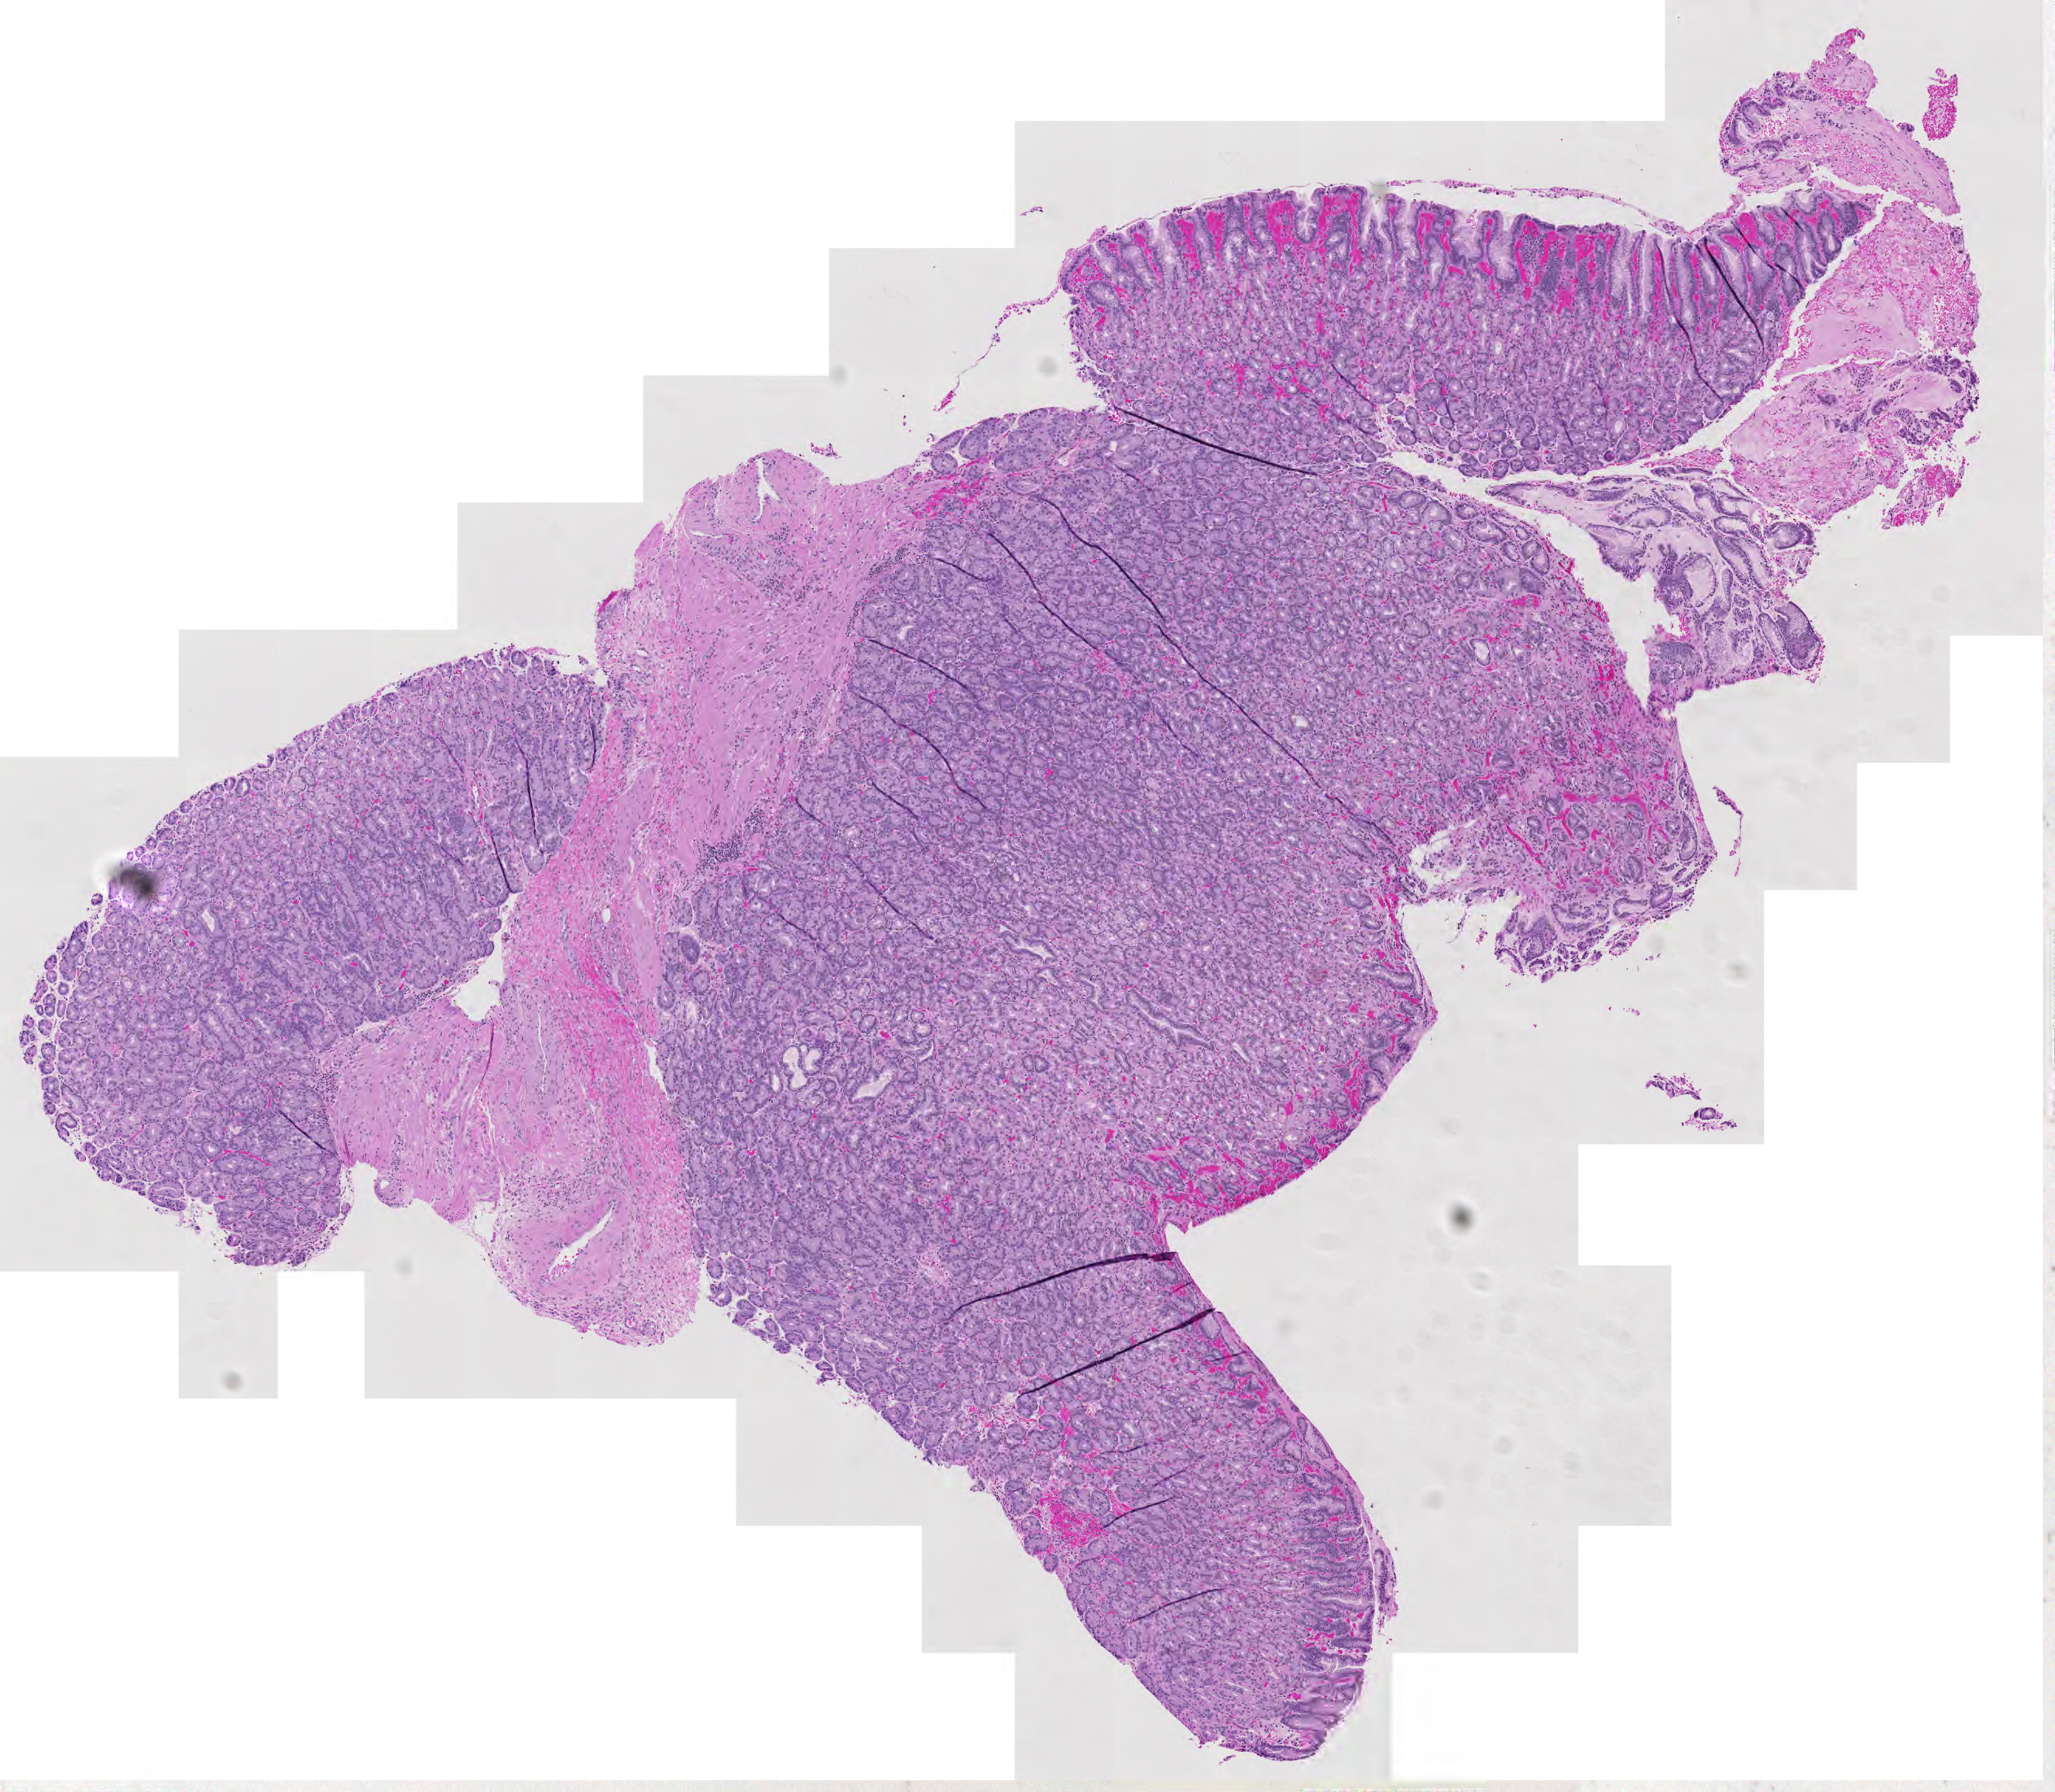
Whole-slide histology image, H&E-stained — low-resolution overview of the scanned area, about 6.8 x 6.0 mm. Patient: male, age 87 years.
Patient diagnosis (cohort enrolment): sarcoma (site not recorded at cohort level).